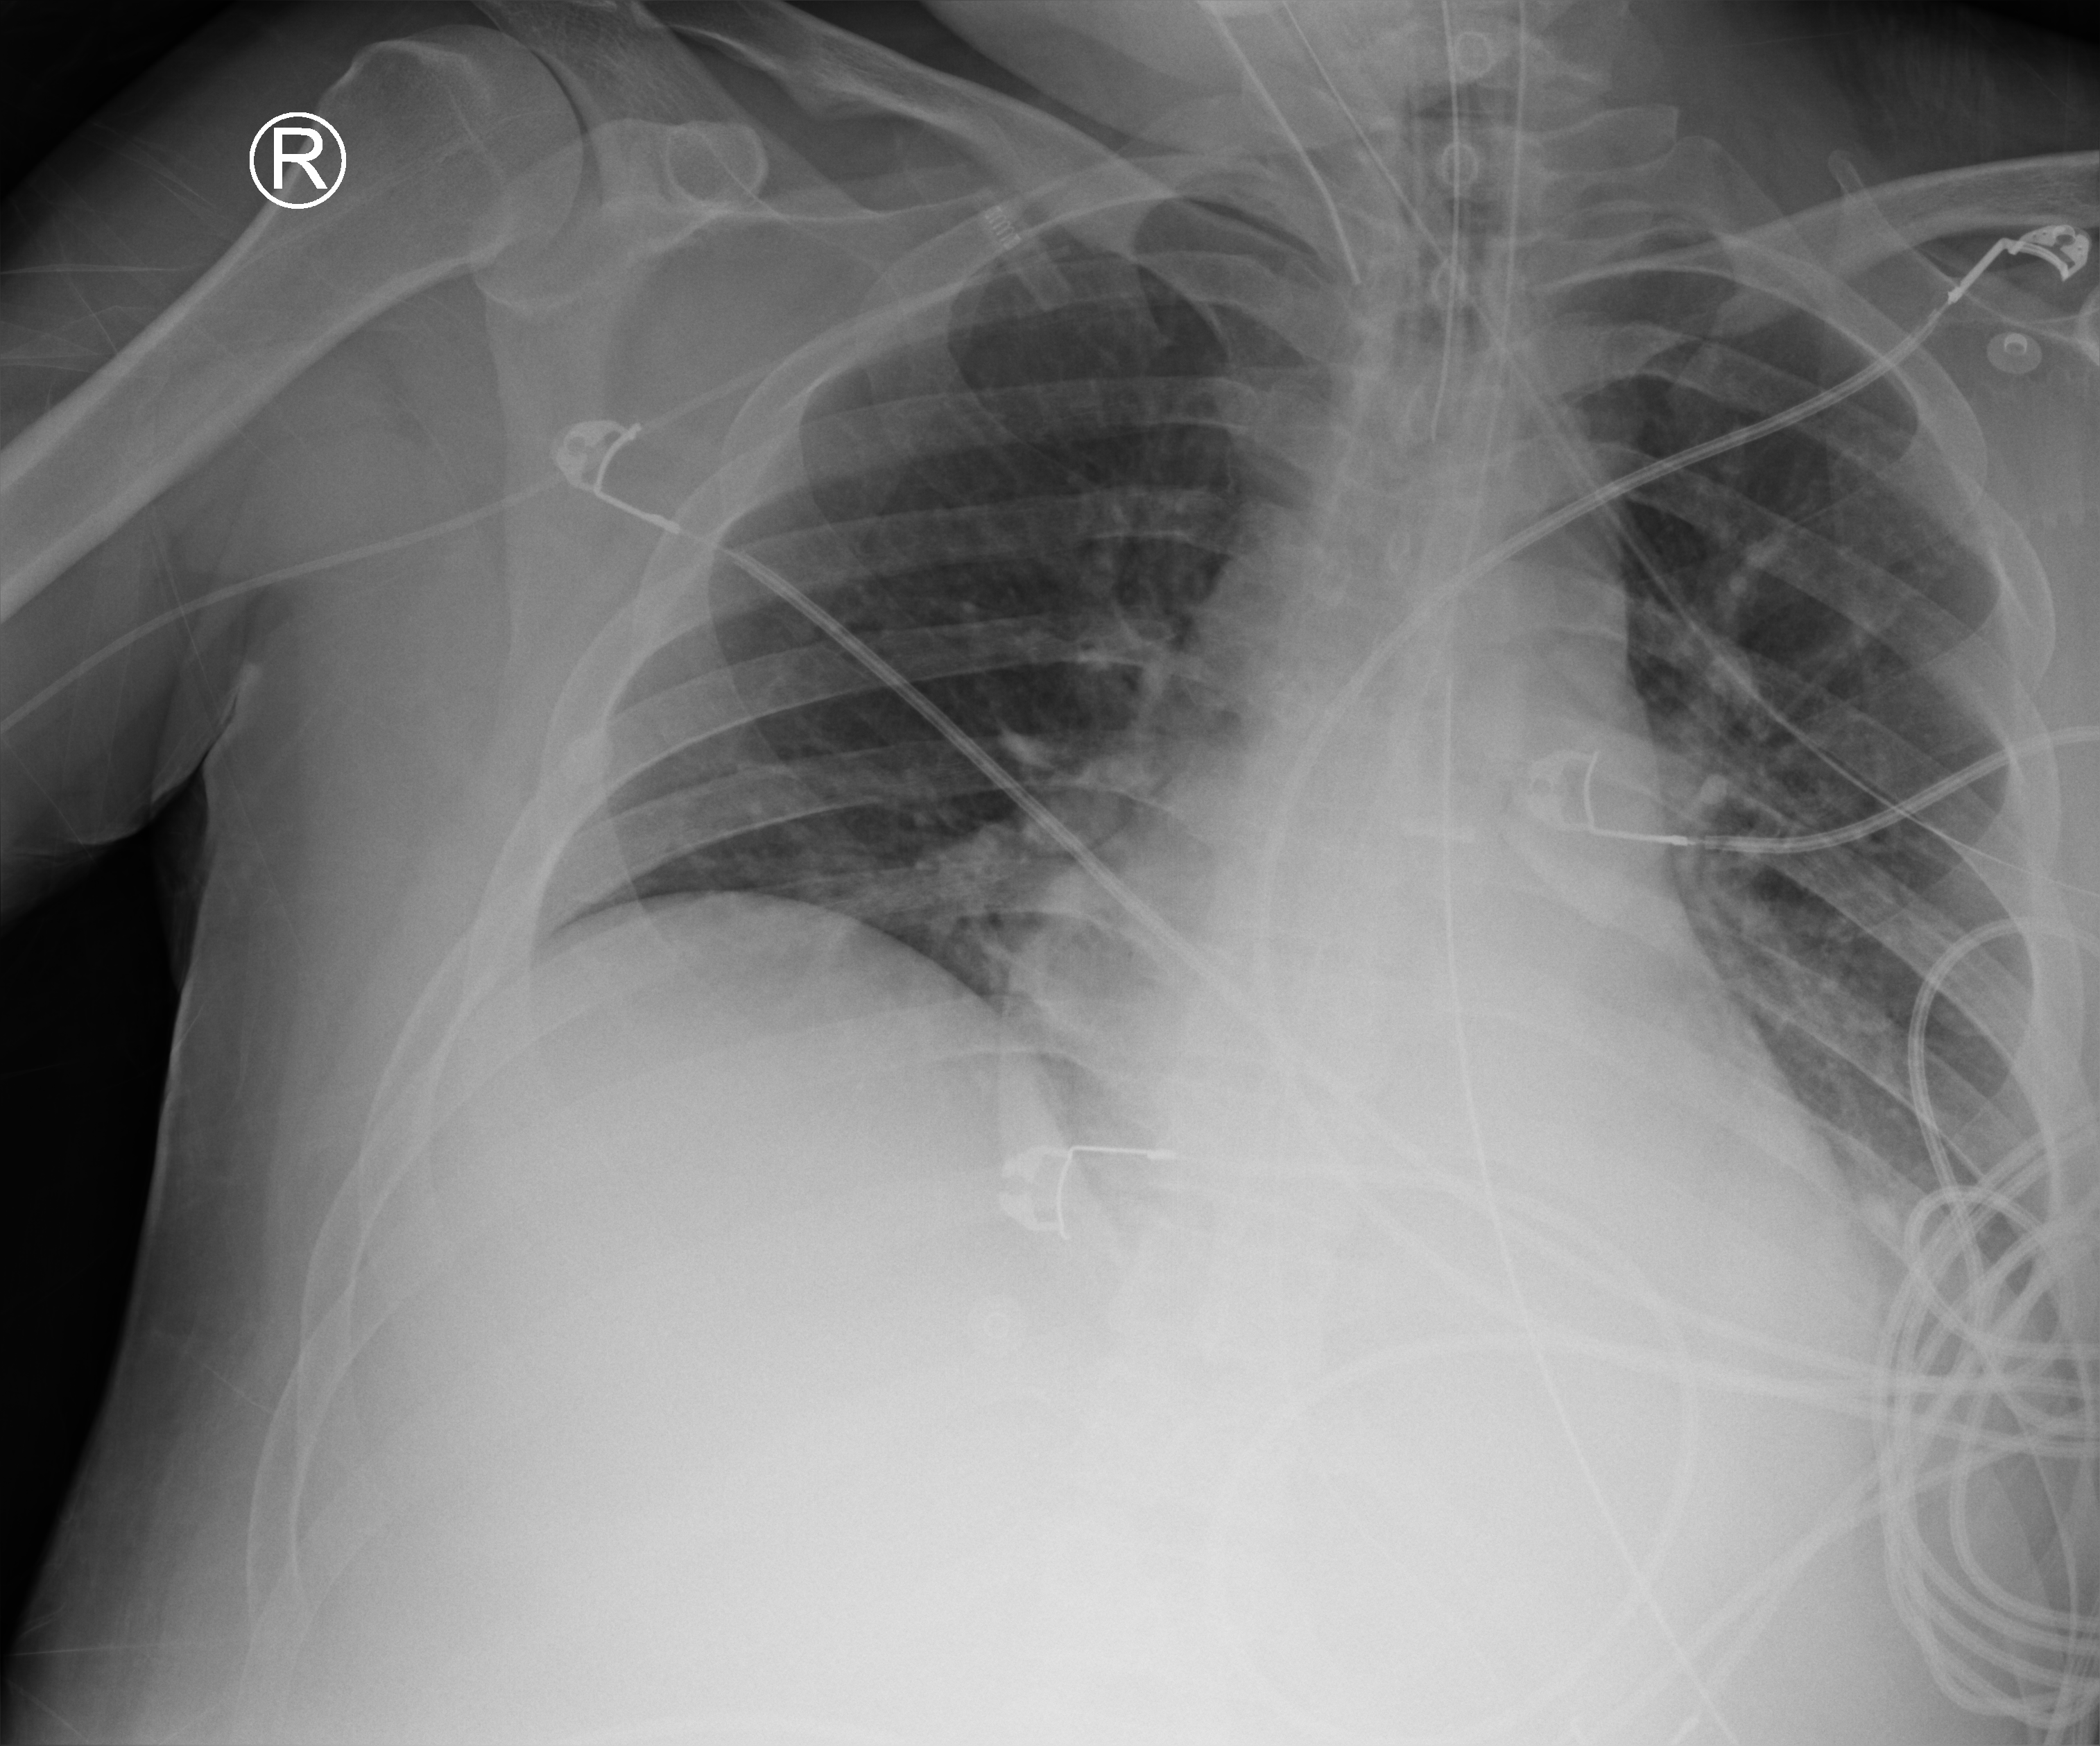
Bedside chest radiograph (computed radiography), anteroposterior (AP) projection. Male patient hospitalised with COVID-19, age 18–59 years.
Hospital-stay facts (about this admission, not read from this image; timing relative to this image not recorded): smoking status (admission record): current; admitted to intensive care during this hospital stay: yes; other chronic lung disease (admission record): no.